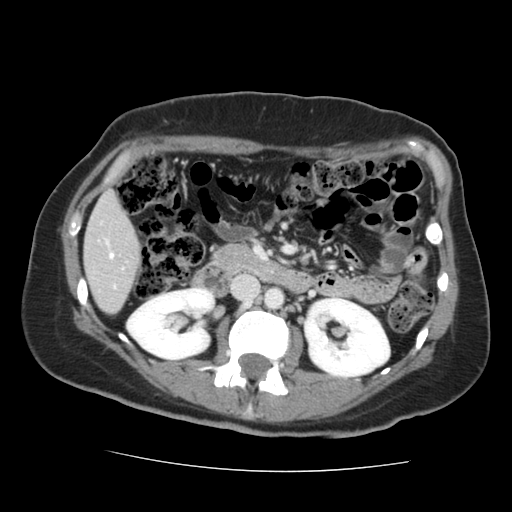
Contrast-enhanced abdominal CT, one axial slice; slice 59 of 144 in the series (ordered by position); intravenous contrast given; soft-tissue window (W 400 / L 40 HU); 2.5 mm slice thickness; 512 × 512 image matrix, field of view 333 × 333 mm. Female patient, age 46 years. From the clinical record (not read from this slice): diagnosis: colorectal cancer liver metastases, imaged before liver resection; multiple liver metastases: no; largest metastasis: 2.8 cm; disease in both lobes: no.
Outlined on this slice (manually delineated by an expert):
- liver: box from (x=85, y=194) to (x=138, y=313) px
- planned liver remnant (the part of the liver to remain after resection): (x=85, y=194)–(x=138, y=251)
- portal vein (with intrahepatic branches): (x=106, y=242)–(x=115, y=288)